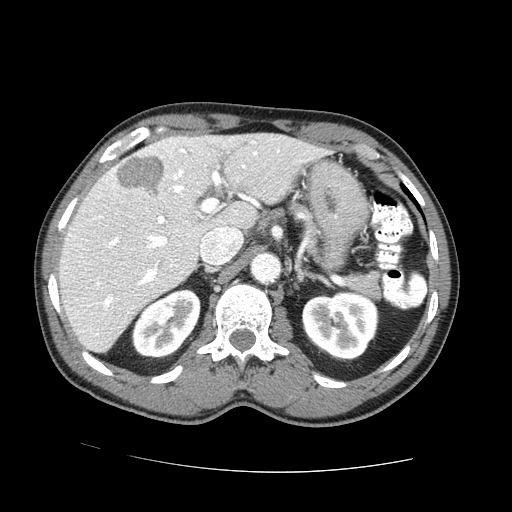
Contrast-enhanced abdominal CT (liver protocol), one axial slice; position 45 of 73 along the scan axis; 100 kVp; one of 2 acquisitions stored at this slice position; soft-tissue window (W 400 / L 40 HU); 2.5 mm slice thickness; 512 × 512 image matrix, field of view 380 × 380 mm. From the clinical record (not read from this slice): diagnosis: hepatocellular carcinoma (patient treated with transarterial chemoembolisation; whether this scan precedes or follows treatment is not stated here); TNM stage (as recorded): Stage-IVA; Child-Pugh class: A; tumour nodularity: uninodular.
Structures marked on this image (semi-automatic segmentation, software-assisted and operator-edited):
- liver parenchyma outside the tumour (the mass and vessels are separate outlines, so this box may not span the whole liver): box from (x=58, y=134) to (x=323, y=352) px
- mass: (x=116, y=155)–(x=164, y=196)
- liver vessels: (x=69, y=140)–(x=280, y=335)